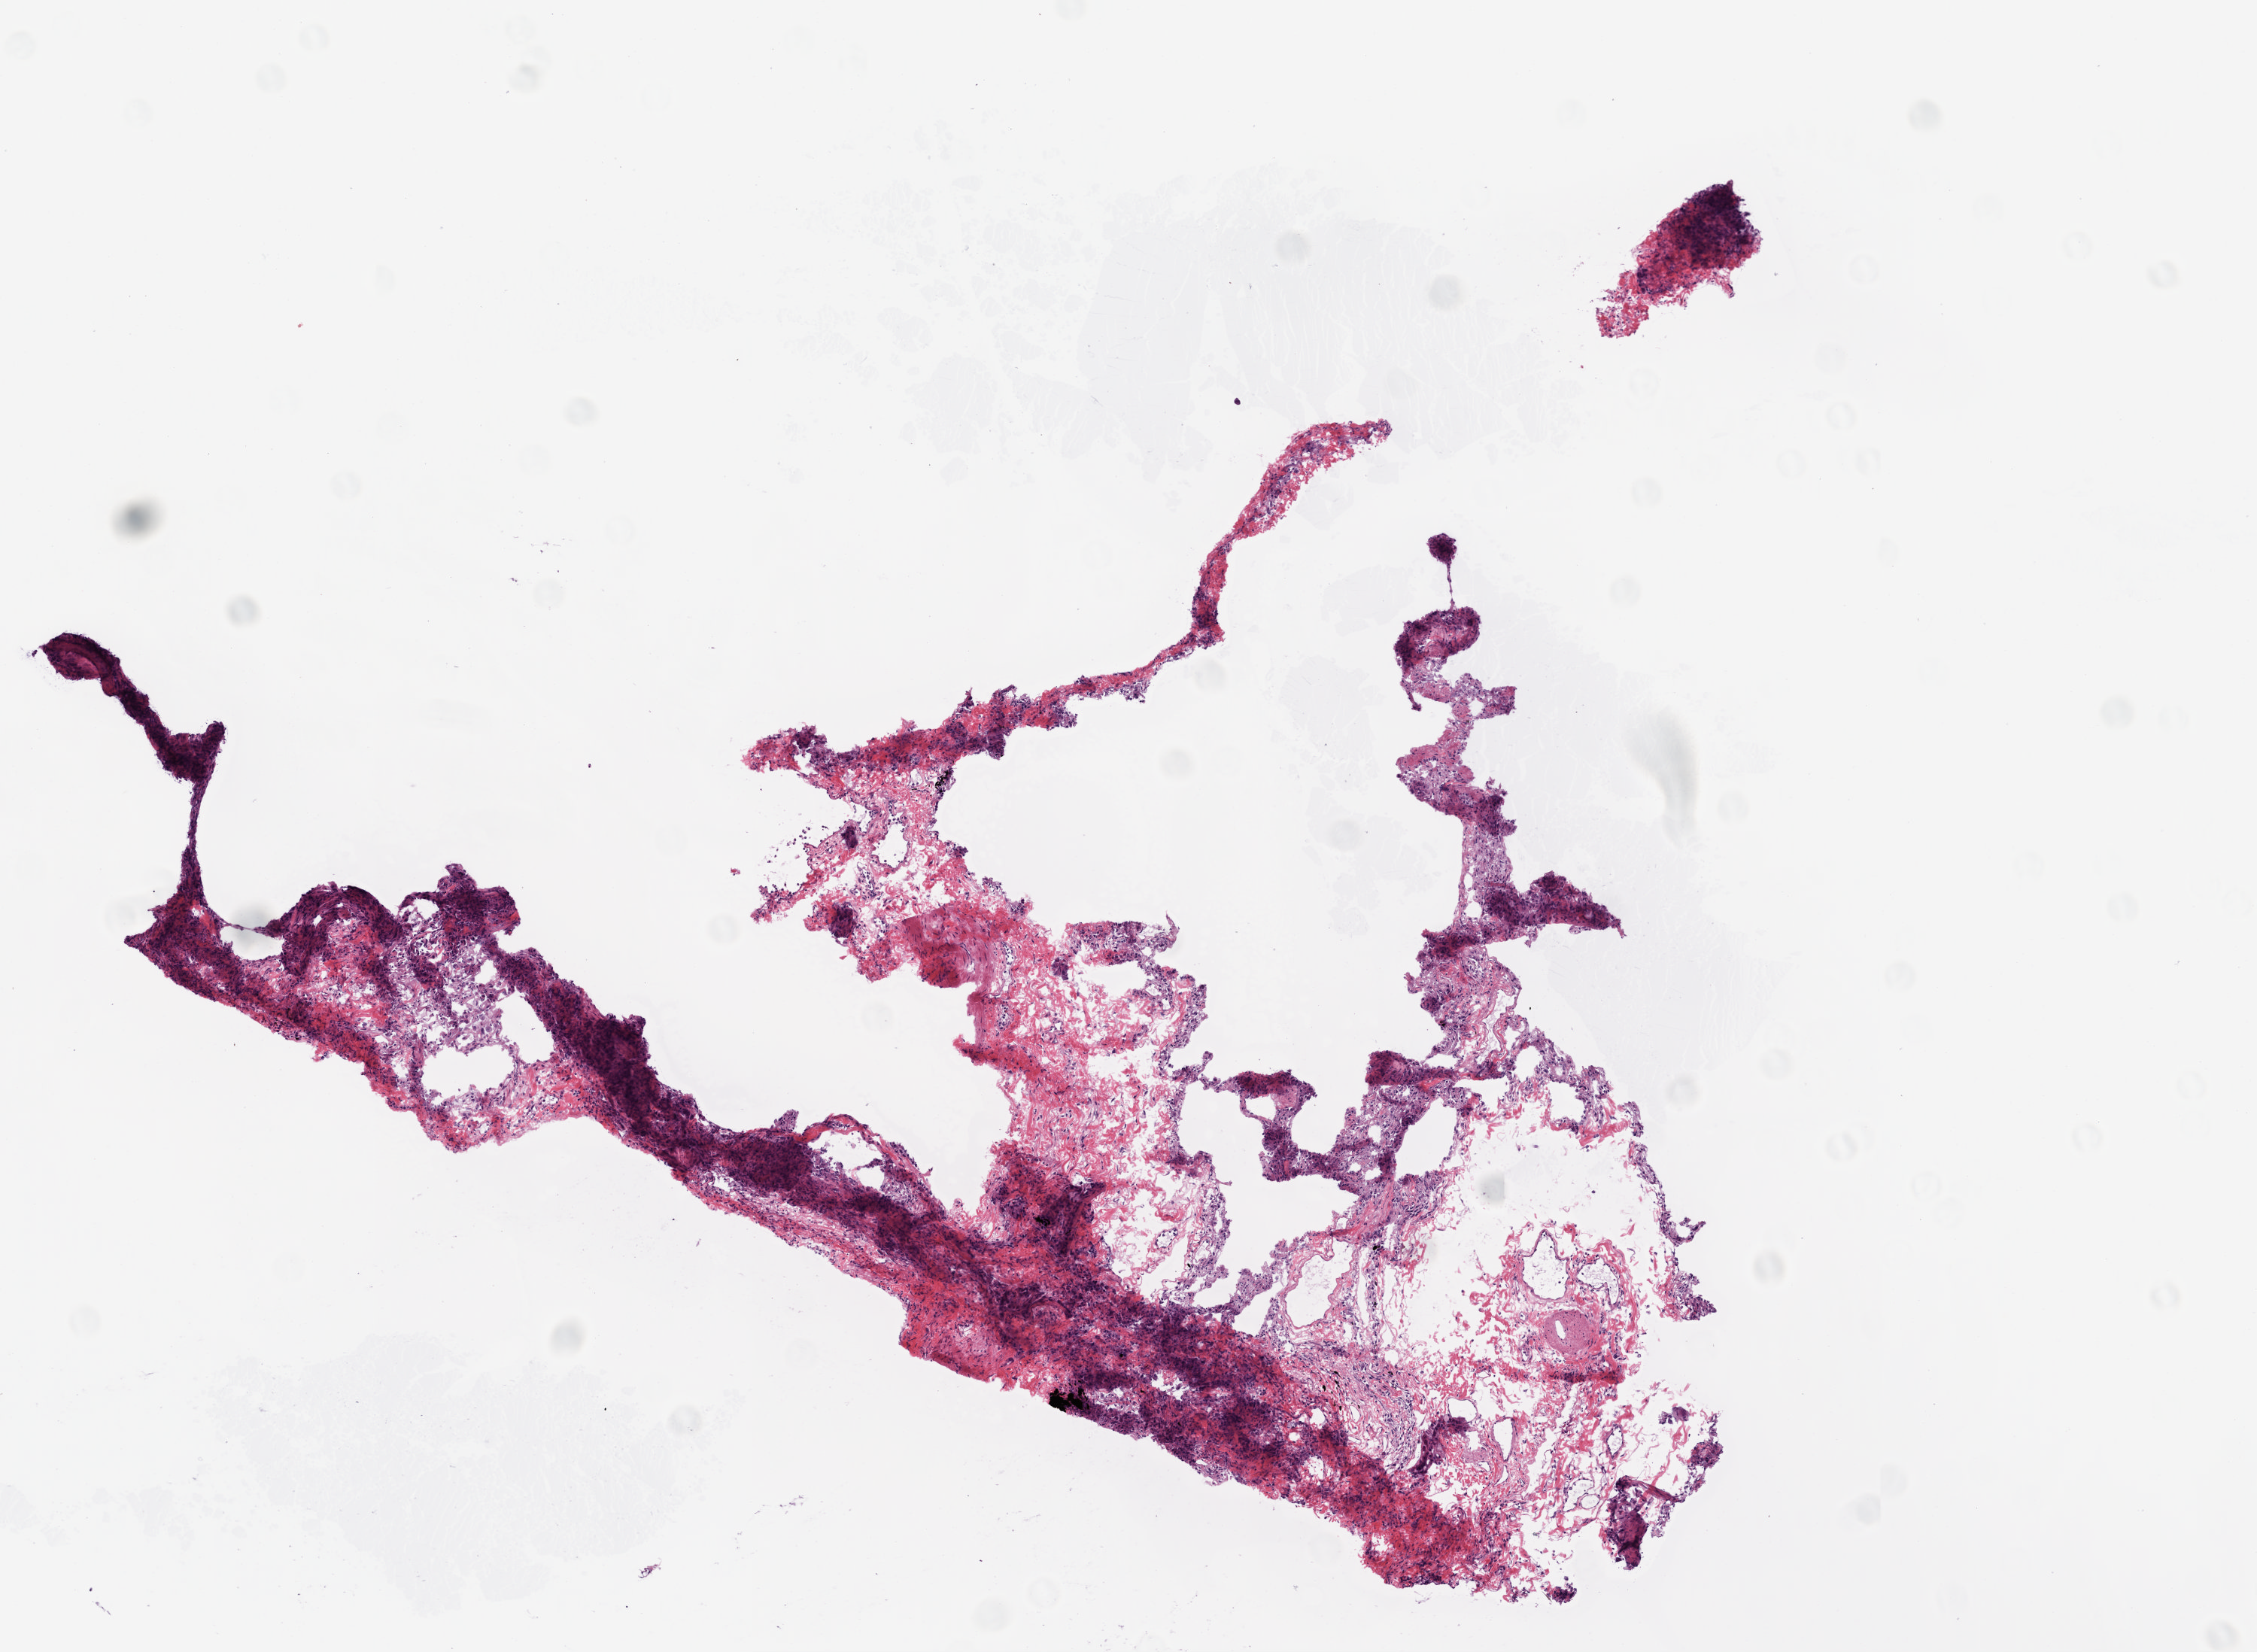
Digitized Hematoxylin and eosin (H&E) stained tissue section (whole slide) — a low-resolution overview of the entire scanned area, about 6.0 x 4.4 mm (from a 20x scan). Frozen section from the top of the tissue portion. Solid tissue normal (non-tumour tissue) sample from the lung. Male, age 72 years at initial diagnosis.
- this section: solid tissue normal sample (biorepository sample class)
- patient diagnosis: Squamous cell carcinoma, NOS (middle lobe, lung)